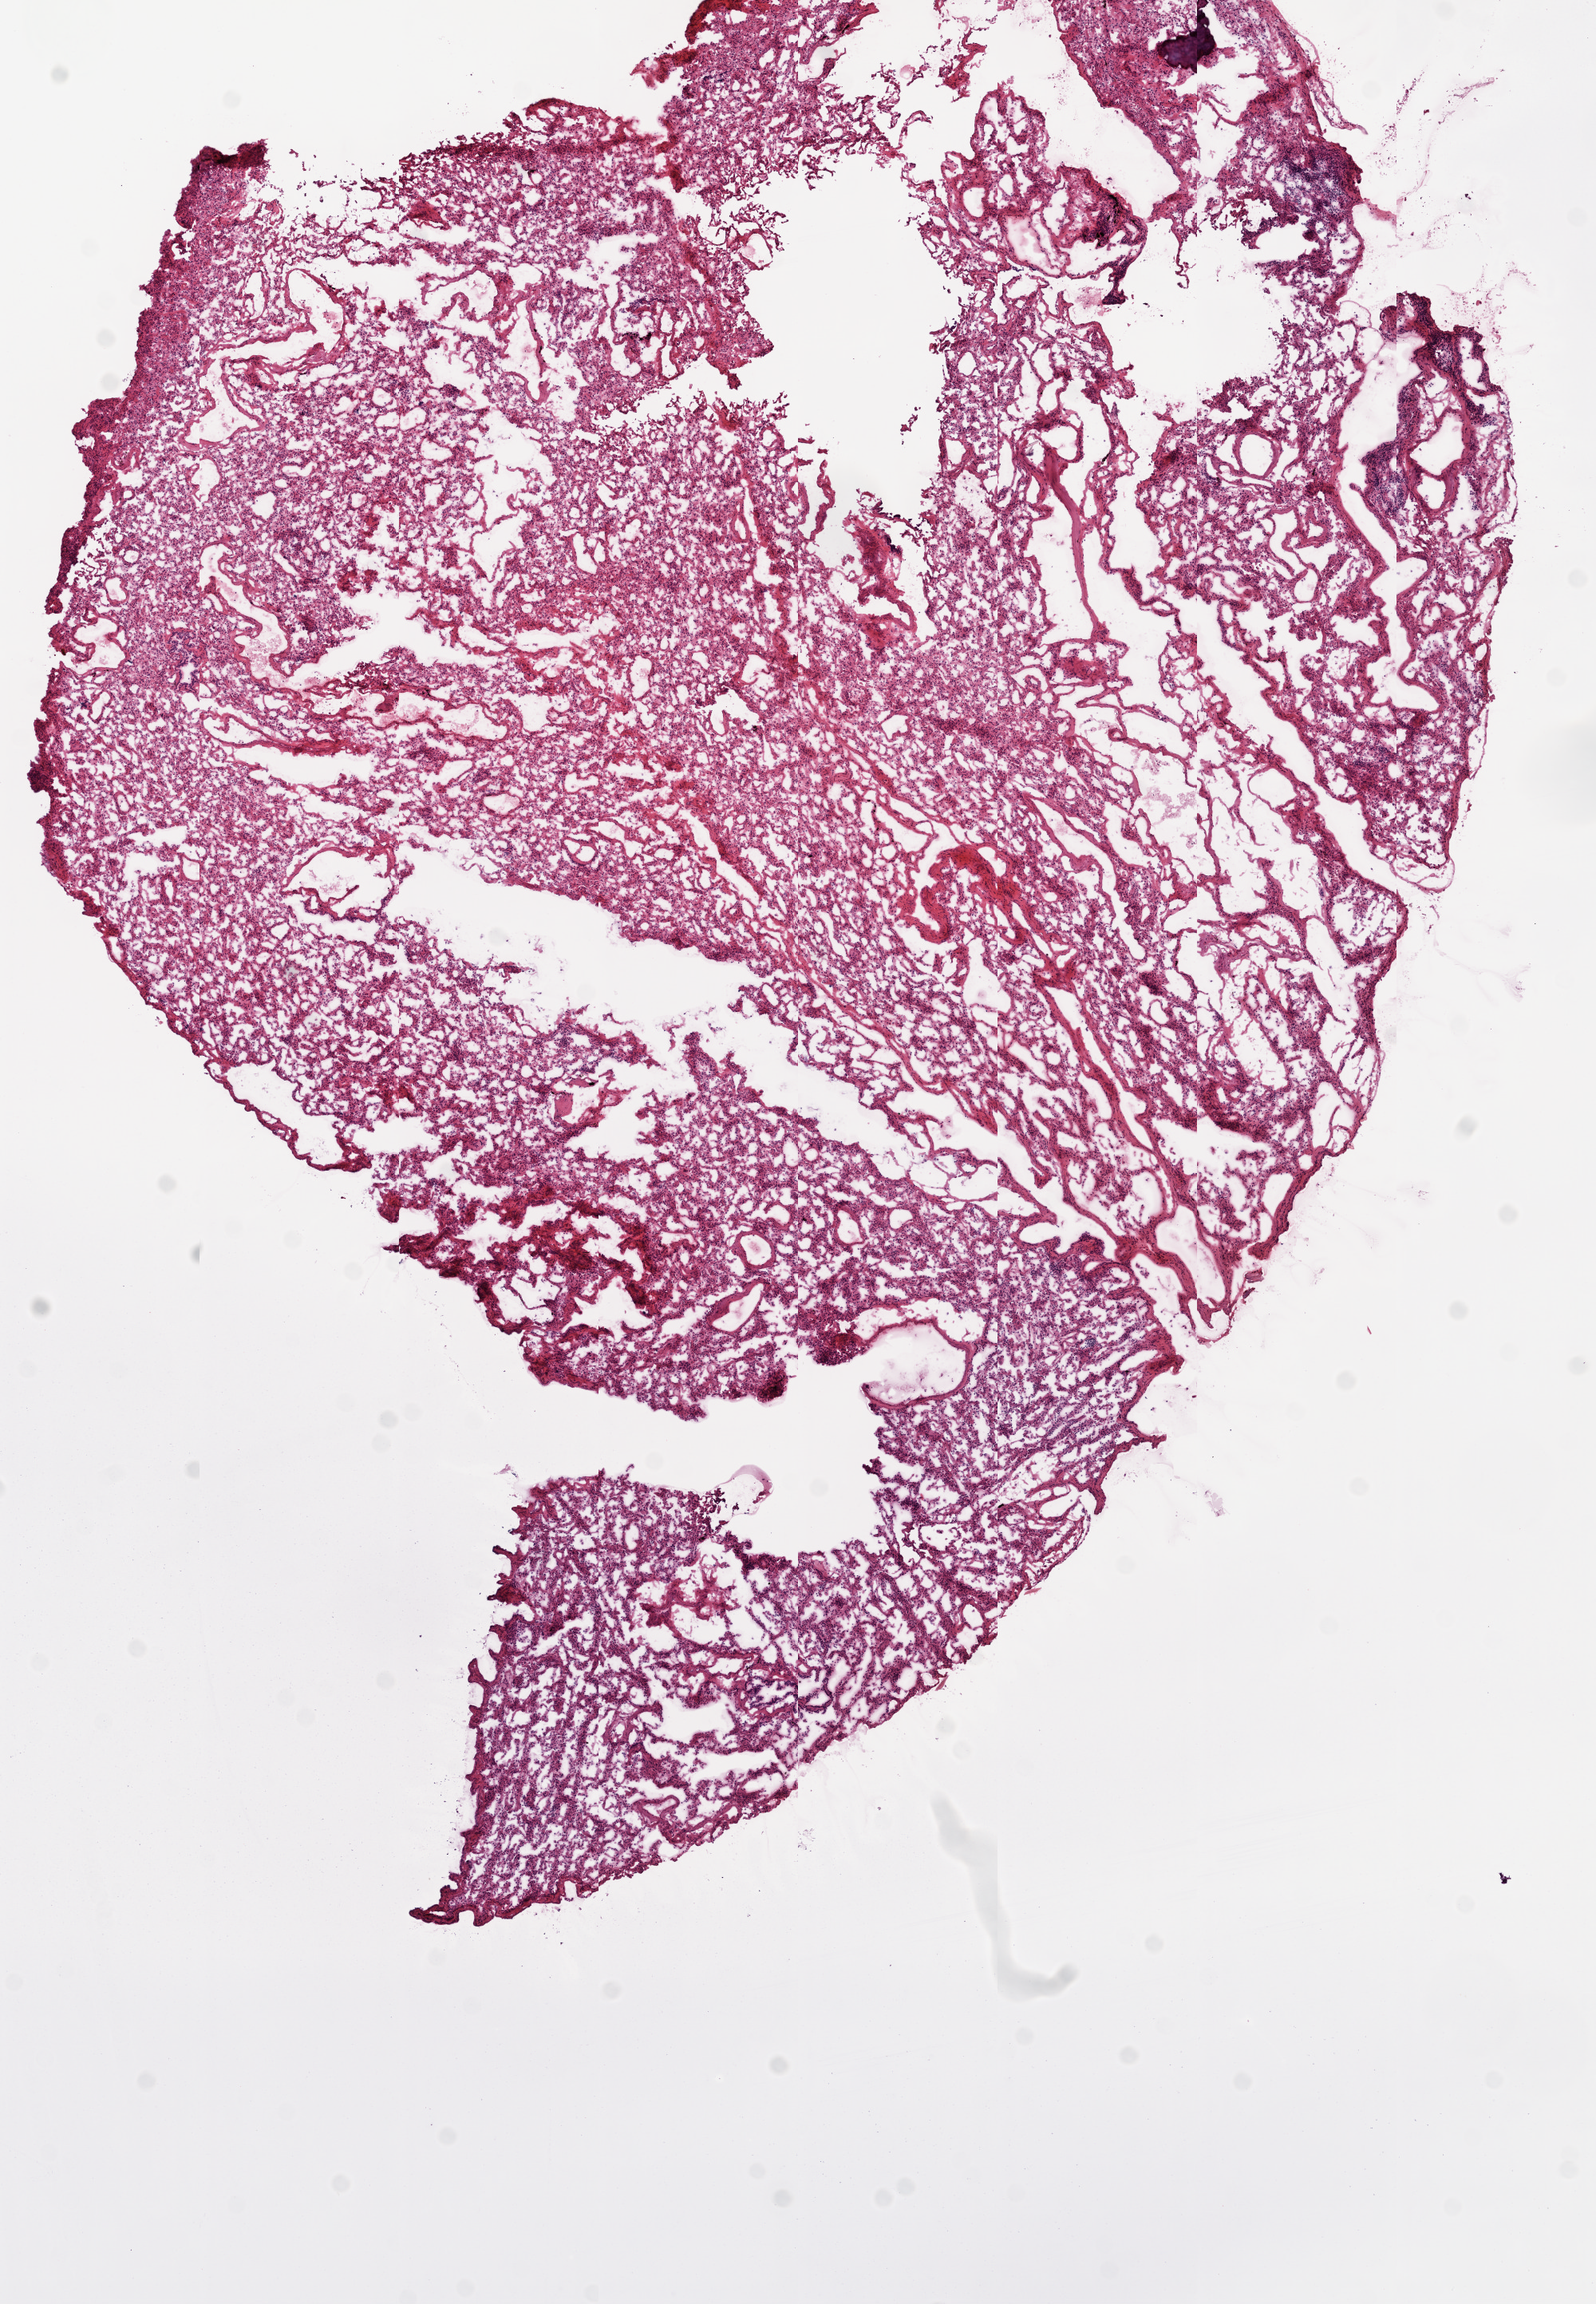
Whole-slide histology image, Hematoxylin and eosin (H&E) stained — a low-resolution overview of the entire scanned area, about 8.0 x 11.6 mm (acquisition: 20x scan). Frozen section. Sample: solid tissue normal (non-tumour tissue), lung. Patient: male, age at initial diagnosis 72 years.
This section: solid tissue normal sample (biorepository sample class). Patient diagnosis: Adenocarcinoma, NOS (lower lobe, lung).